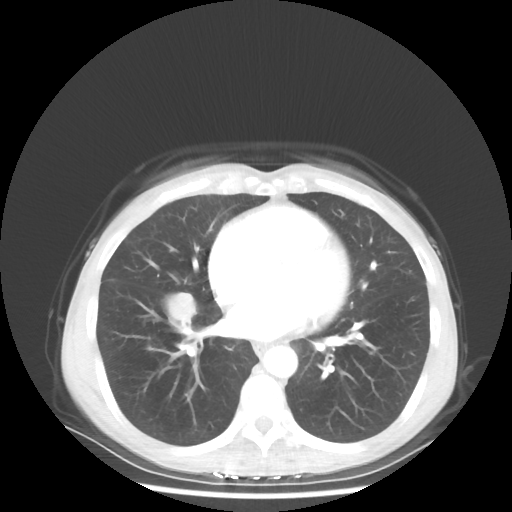
Chest CT, one axial slice. Position 24 of 56 along the scan axis. Lung window (W 1500 / L -600 HU). 5 mm slice thickness. 512 × 512 image matrix, field of view 360 × 360 mm. Patient: female, 57 years. Case-level facts recorded for this patient, not image findings: clinical TNM (as recorded): T1c N3 M1a.
Structures marked on this image (bounding box drawn by a radiologist):
- lung tumour (recorded histology: adenocarcinoma): box from (x=163, y=292) to (x=203, y=331) px